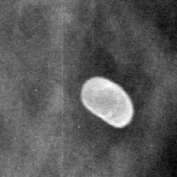
Cropped region of a digitized screen-film mammogram centred on a radiologist-marked abnormality; left breast; MLO view; BI-RADS breast density category 2 (scale 1–4).
Finding: calcifications, morphology lucent center; BI-RADS assessment category 2; benign without callback (not worked up further).